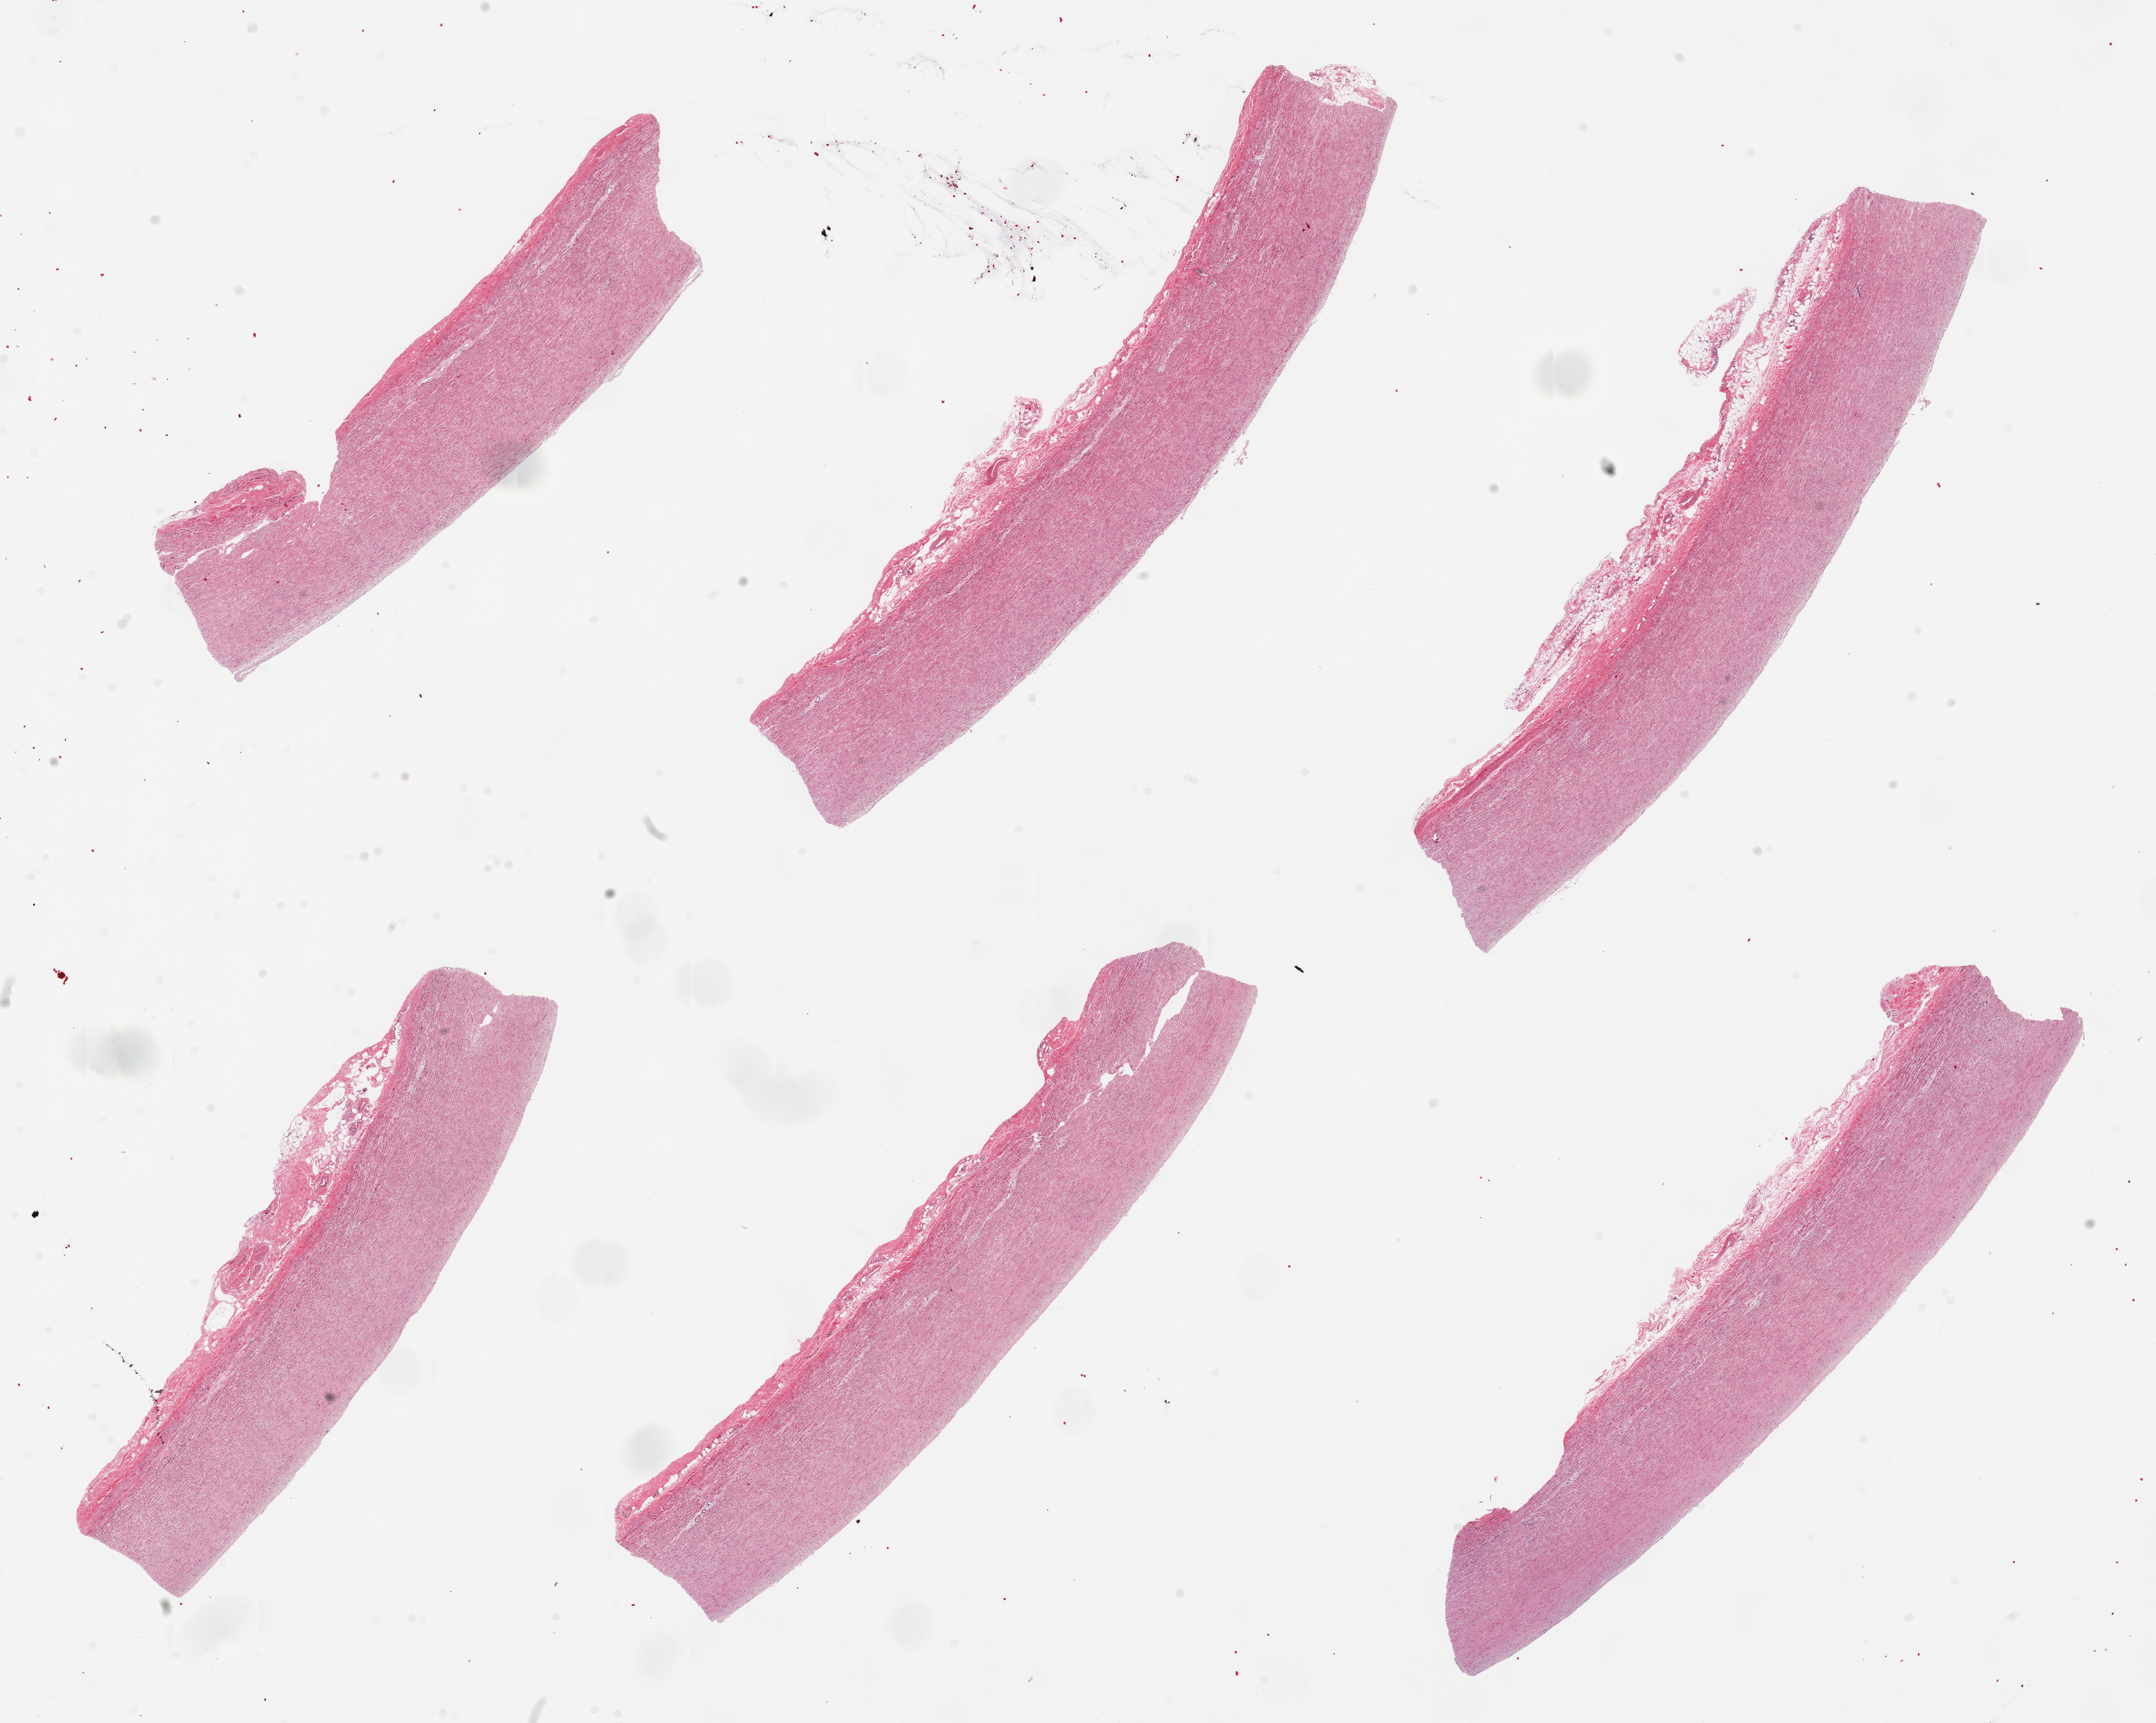
Digitized haematoxylin and eosin-stained section — shown as a low-resolution overview of the whole scanned area (about 24.6 x 19.7 mm, slide scanned at 20x). PAXgene-fixed paraffin-embedded (PFPE) section. Section of aorta (target tissue). Tissue donor sample.
Review note (as recorded): 6 pieces.